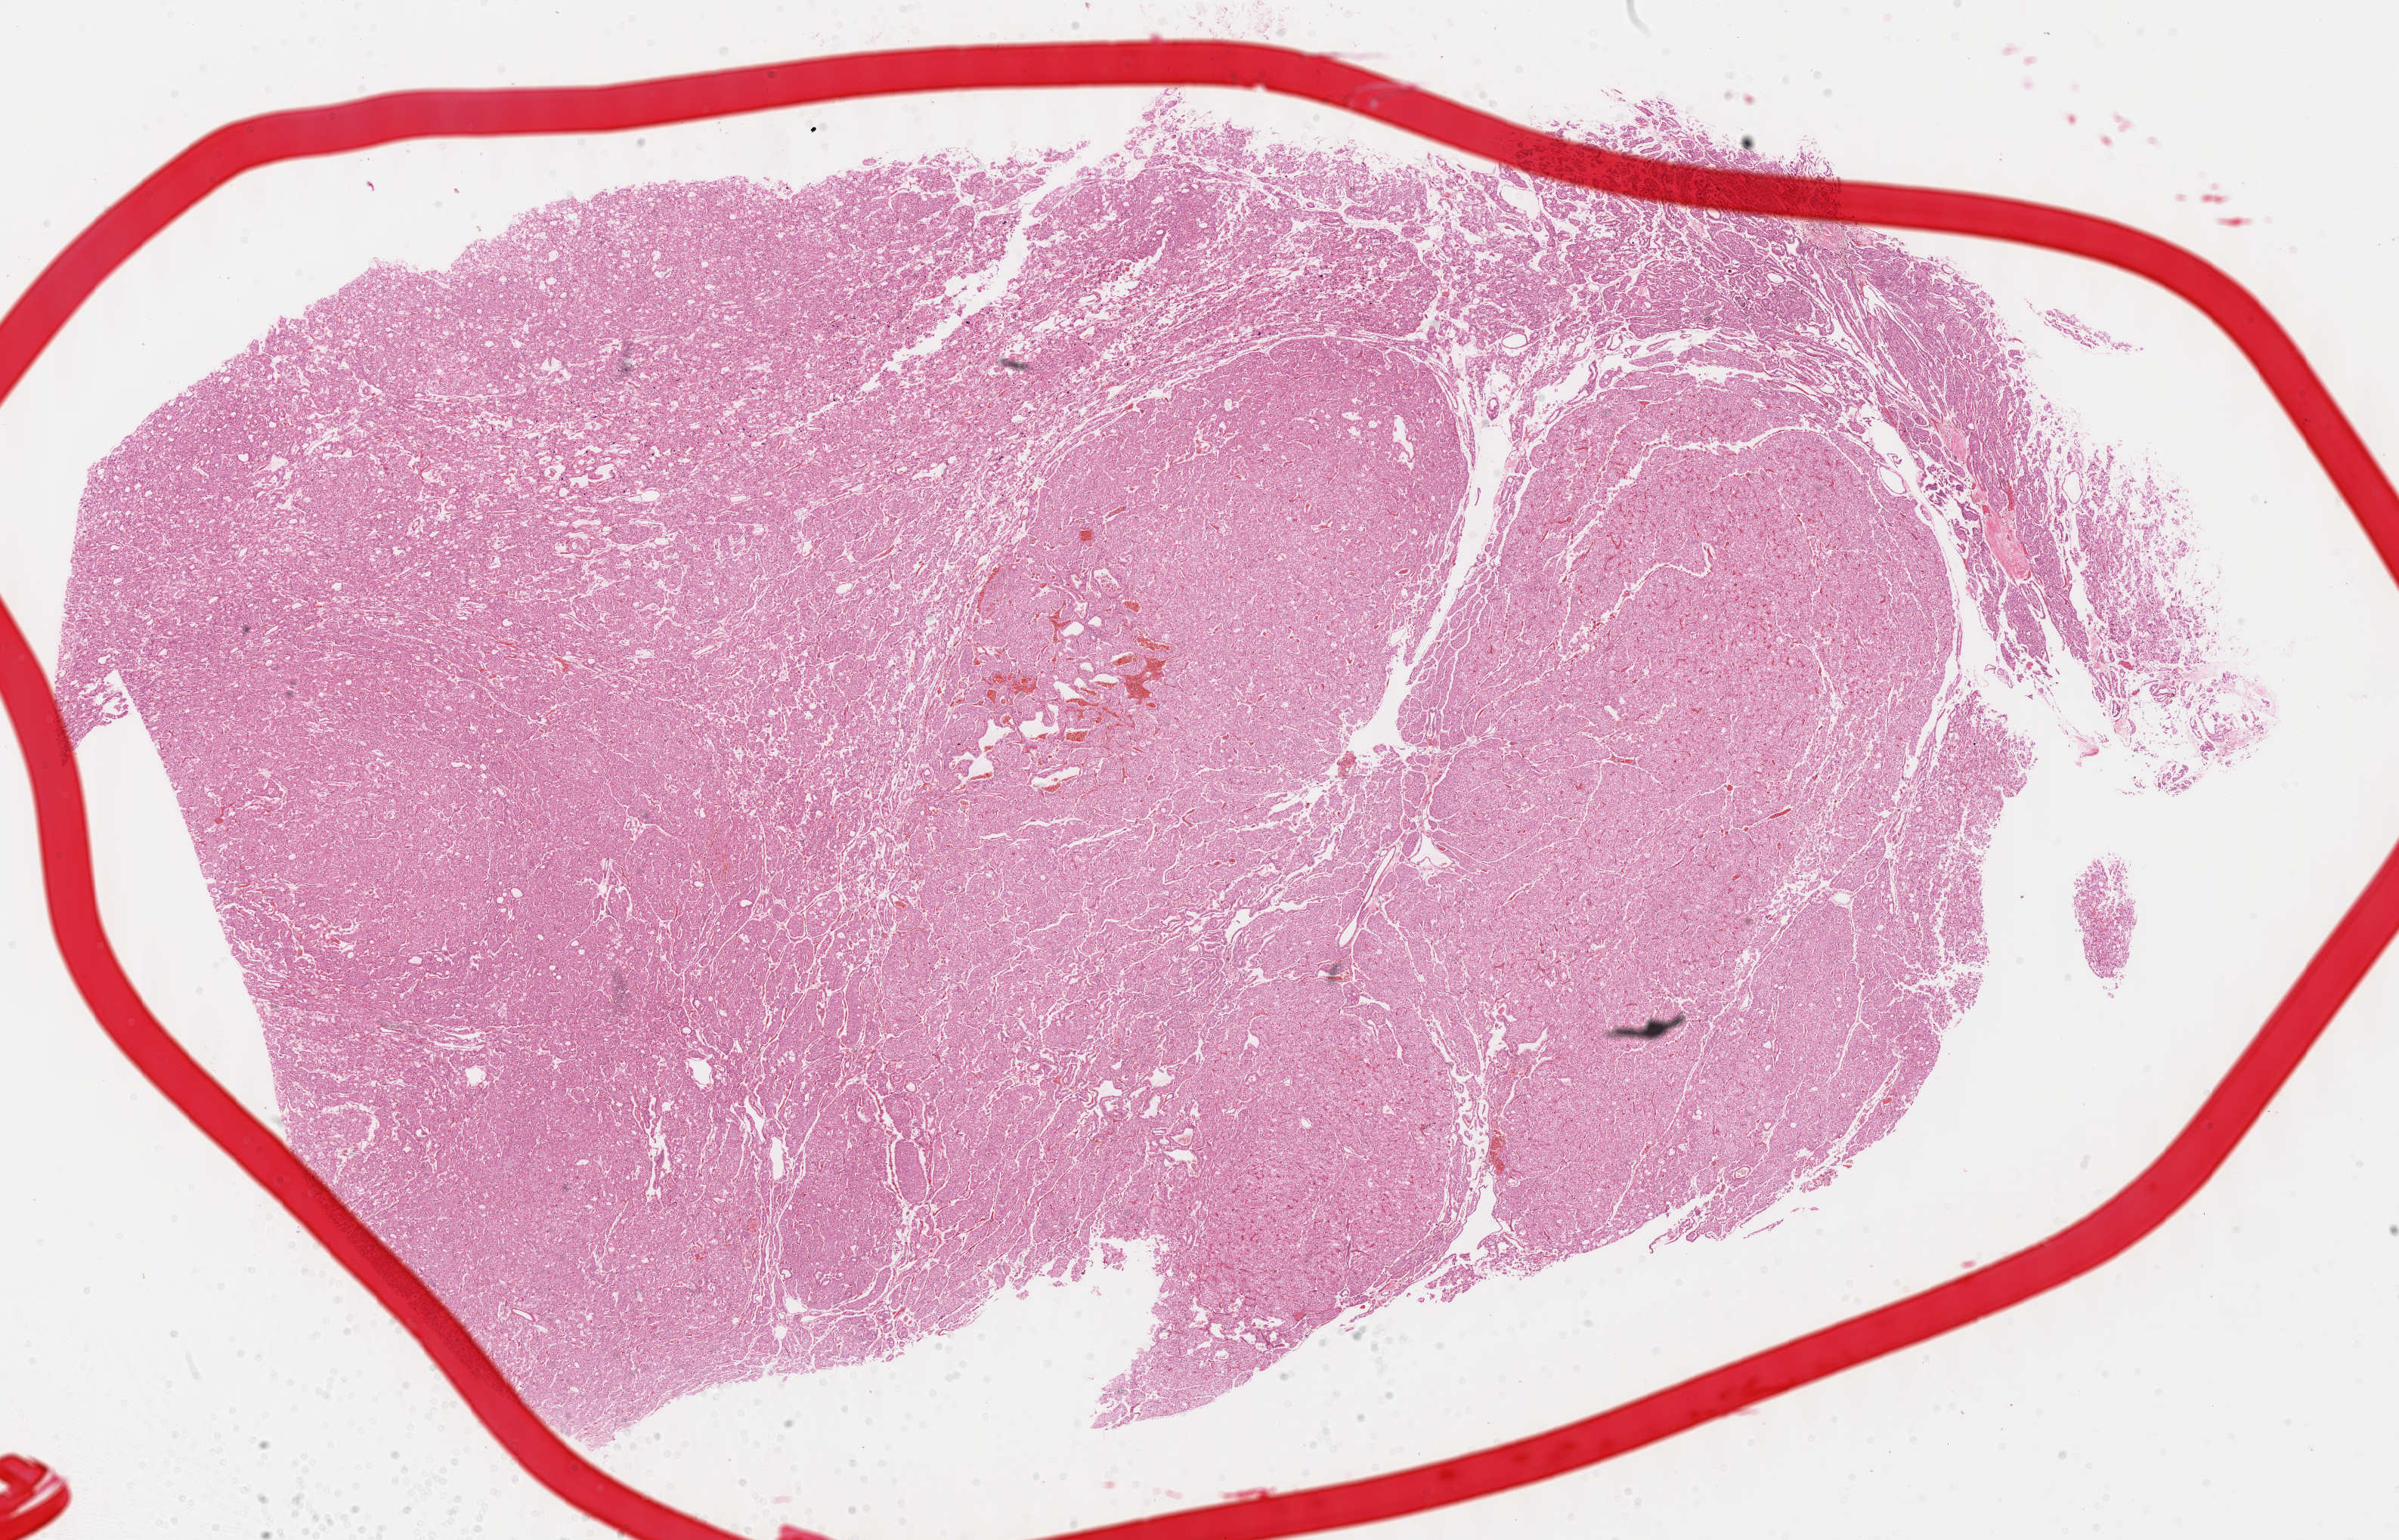
Hematoxylin and eosin (H&E) stained whole-slide image, whole scanned area (about 25.7 x 16.5 mm, acquisition: 40x scan) shown as a low-resolution overview; formalin-fixed paraffin-embedded (FFPE) diagnostic section; kidney, primary tumour sample. Patient: male, age at initial diagnosis 47 years. Slide review estimates, as recorded: tumour cells 94%, tumour nuclei 97%, normal cells 0%, stromal cells 6%, necrosis 0%. Inflammatory infiltration, as recorded: lymphocyte infiltration 2%, monocyte infiltration 0%, neutrophil infiltration 0%.
AJCC pathologic stage: I. Diagnosis: Renal cell carcinoma, chromophobe type.